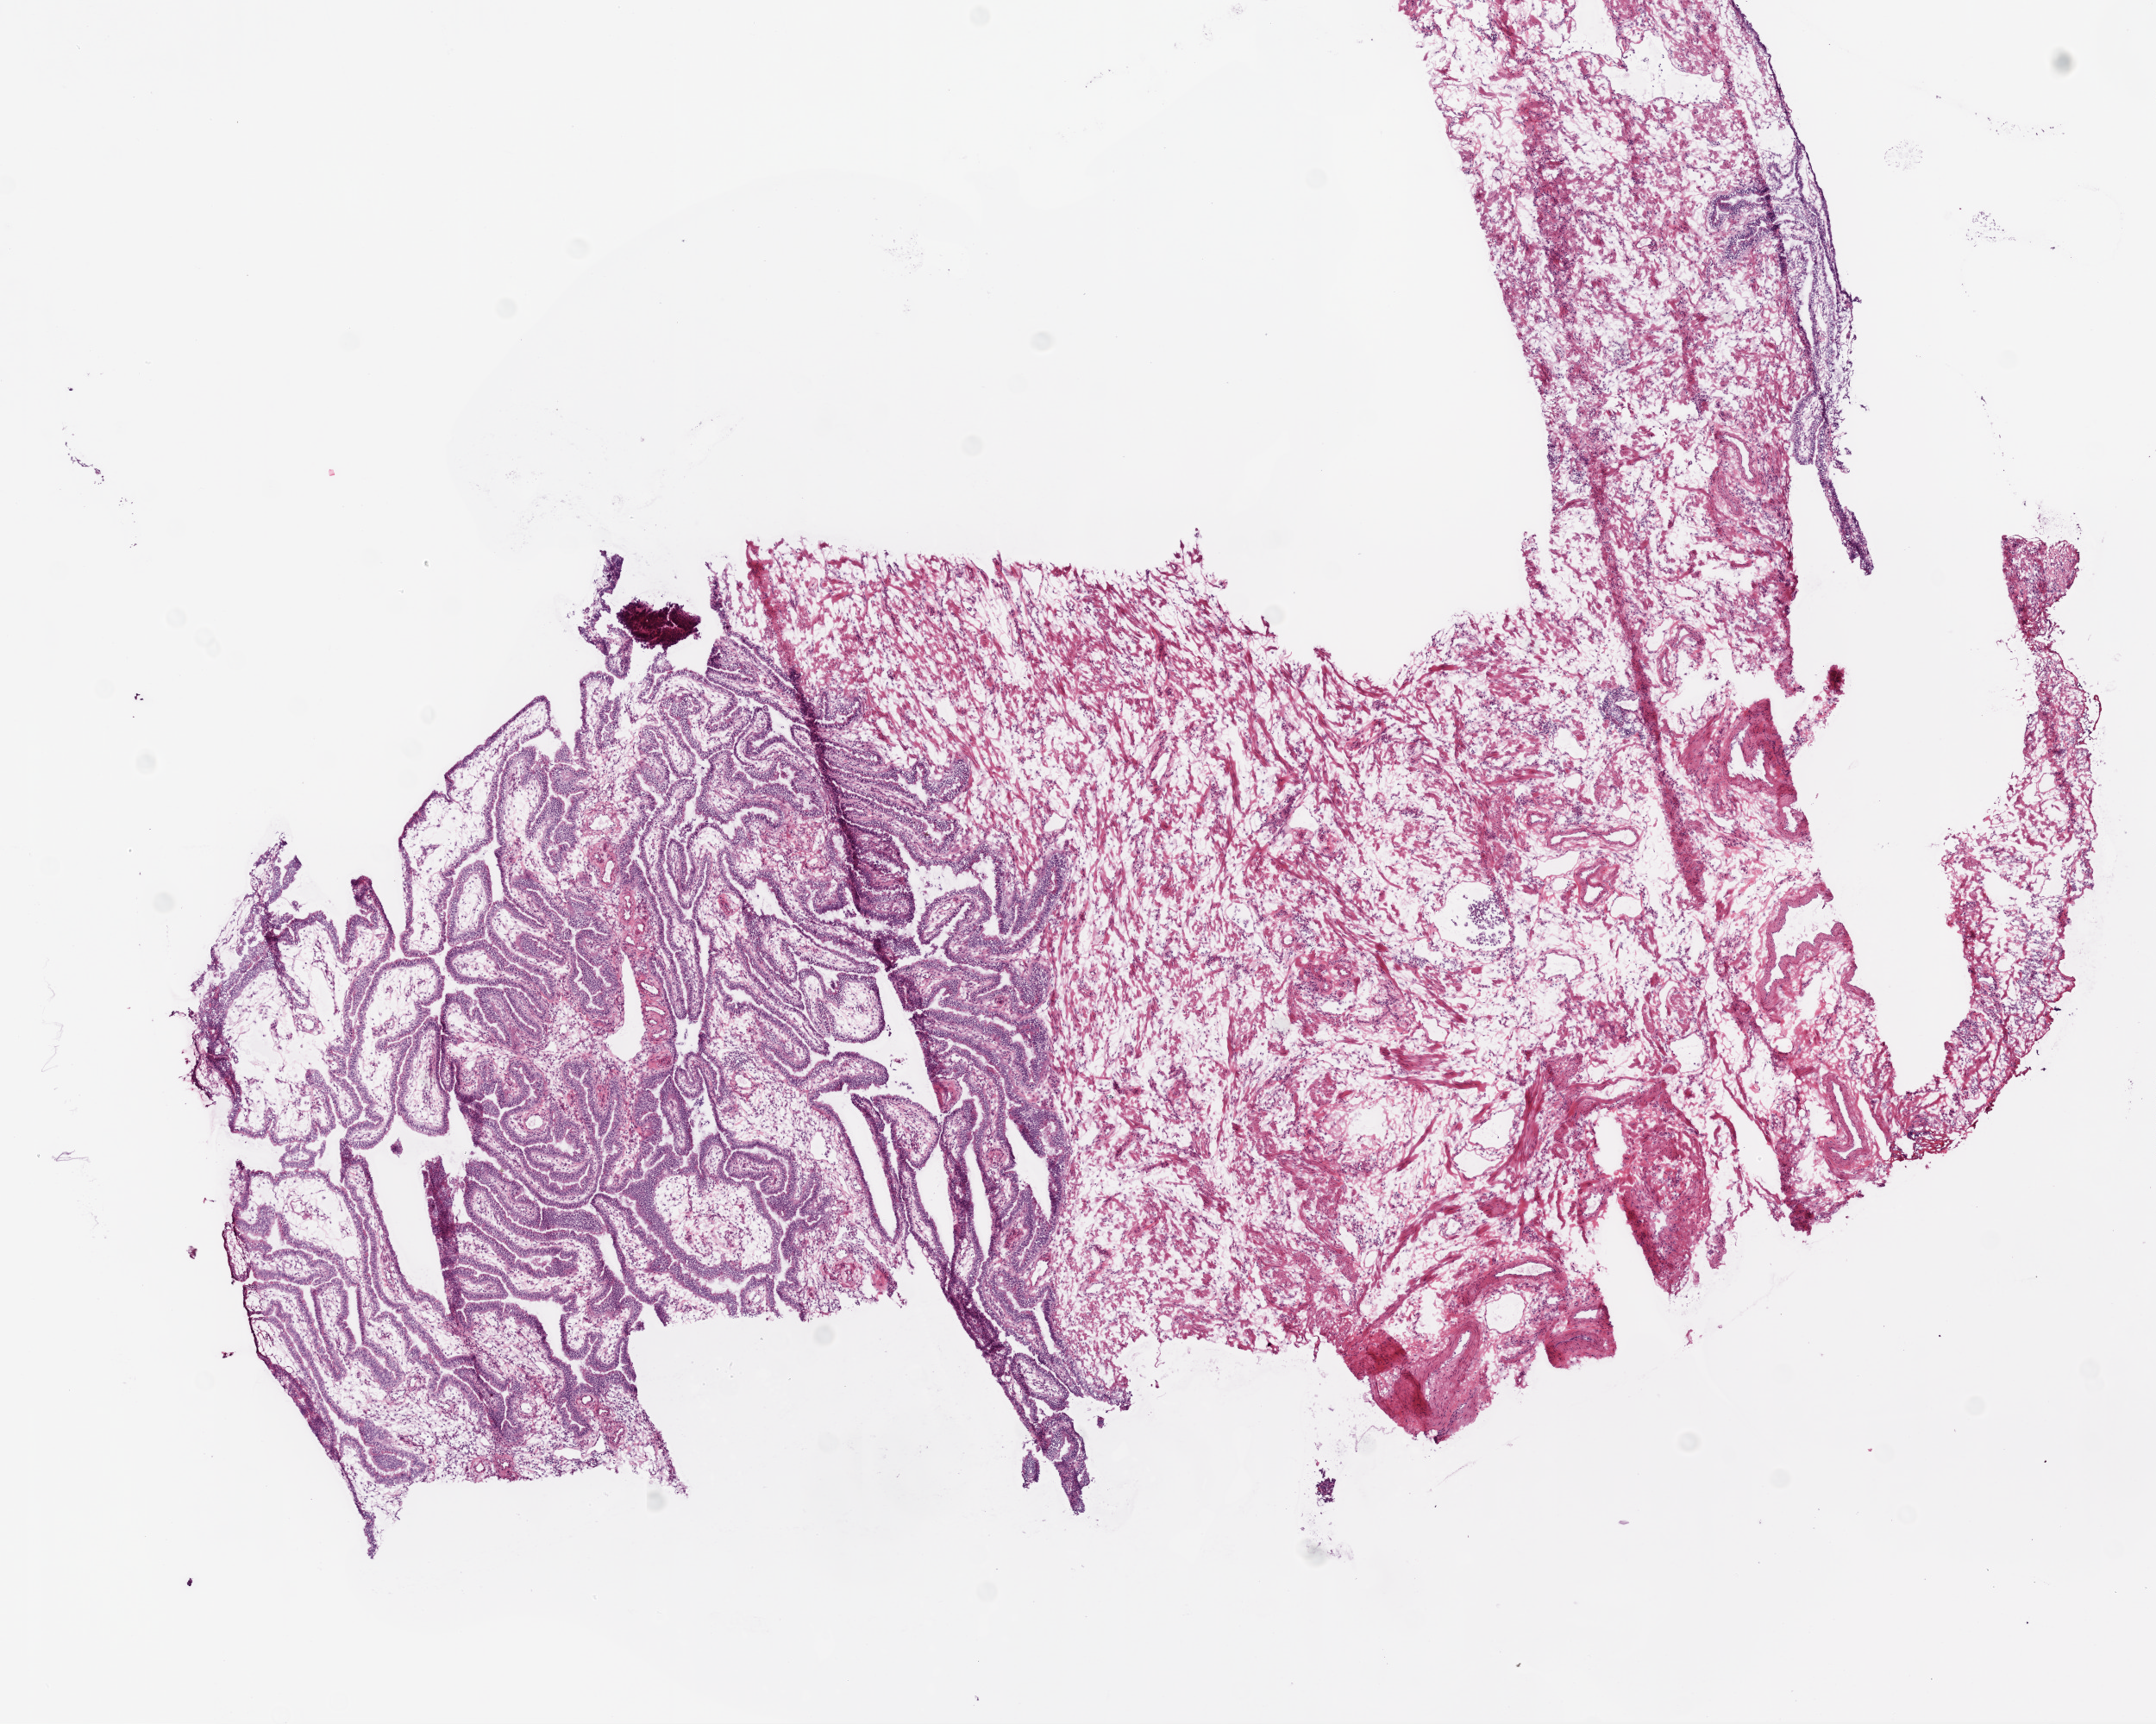
Digitized H&E tissue section (whole slide) — low-resolution overview of the scanned area, about 10.0 x 8.0 mm (from a 20x scan); frozen section; solid tissue normal (non-tumour tissue) sample from the ovary. Female patient; age at initial diagnosis 48 years.
This section: solid tissue normal (non-tumour) sample from the same patient. Patient diagnosis: Serous cystadenocarcinoma, NOS.